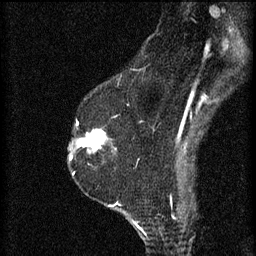
Breast MRI (dynamic contrast-enhanced), one sagittal slice. Position 44 of 60 along the scan axis. 3 images stored at this slice position (order not interpretable as contrast timing). 1.5 T. TE 4.2 ms, TR 8.2 ms. 256 × 256 image matrix. Female patient, age 60 years.
Outlined on this slice (semi-automatically segmented with operator editing):
- analysis volume of interest (the breast-tissue region the enhancement analysis was run in; not a lesion): bounding box [x1, y1, x2, y2] px = [74, 124, 113, 155]
- tumour enhancement mask (voxels above the 70 % enhancement threshold inside the analysis volume of interest): [76, 124, 107, 151]